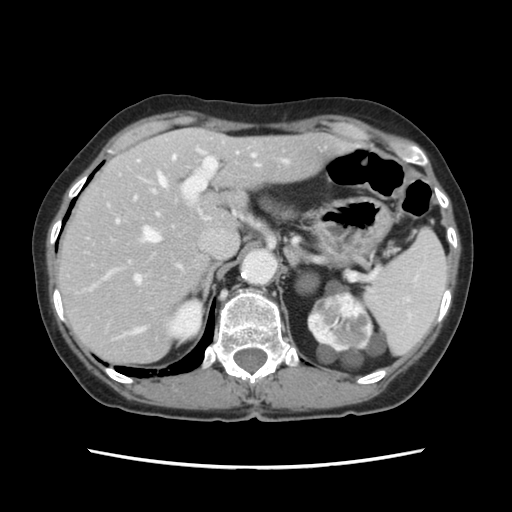
Contrast-enhanced abdominal CT, one axial slice. Position 84 of 120 along the scan axis. Soft-tissue window (W 400 / L 40 HU). 2.5 mm slice thickness. 512 × 512 image matrix. Female patient, age 70 years. Case-level facts recorded for this patient, not image findings: diagnosis: colorectal cancer liver metastases, imaged before liver resection; multiple liver metastases: no; largest metastasis: 2.5 cm; disease in both lobes: no.
Annotated regions visible in this slice (manually delineated by an expert):
- hepatic veins: box from (x=144, y=155) to (x=259, y=242) px
- liver: (x=58, y=128)–(x=343, y=363)
- planned liver remnant (the part of the liver to remain after resection): (x=104, y=127)–(x=343, y=291)
- portal vein (with intrahepatic branches): (x=105, y=149)–(x=288, y=284)